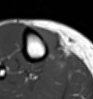
MRI of an extremity soft-tissue mass, one axial slice. Slice 21 of 54 in the series (ordered by position). MR volume resampled by the dataset authors to the PET/CT grid (not the native acquisition matrix). 93 × 99 image matrix. Female patient. From the clinical record (not read from this slice): histological type: undifferentiated – high grade; grade: high; site of the primary tumour: right thigh.
Outlined on this slice (expert contour drawn on MRI and transferred to this co-registered scan by the dataset authors):
- gross tumour volume (mass): bounding box <34,27,62,58> (left, top, right, bottom; pixels)